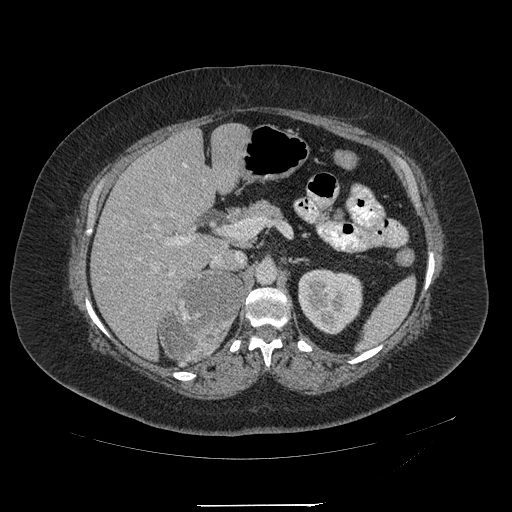
Contrast-enhanced abdominal CT, one axial slice; slice 127 of 217 in the series (ordered by position); reconstruction kernel STANDARD; 120 kVp; soft-tissue window (W 400 / L 40 HU); 1.25 mm slice thickness; 512 × 512 image matrix, field of view 453 × 453 mm. Patient: female, 55 years. Case-level facts recorded for this patient, not image findings: diagnosis: adrenocortical carcinoma; tumour side: right adrenal.
Structures marked on this image (semi-automatic segmentation, software-assisted and operator-edited):
- mass: bounding box [x1, y1, x2, y2] px = [159, 271, 242, 361]